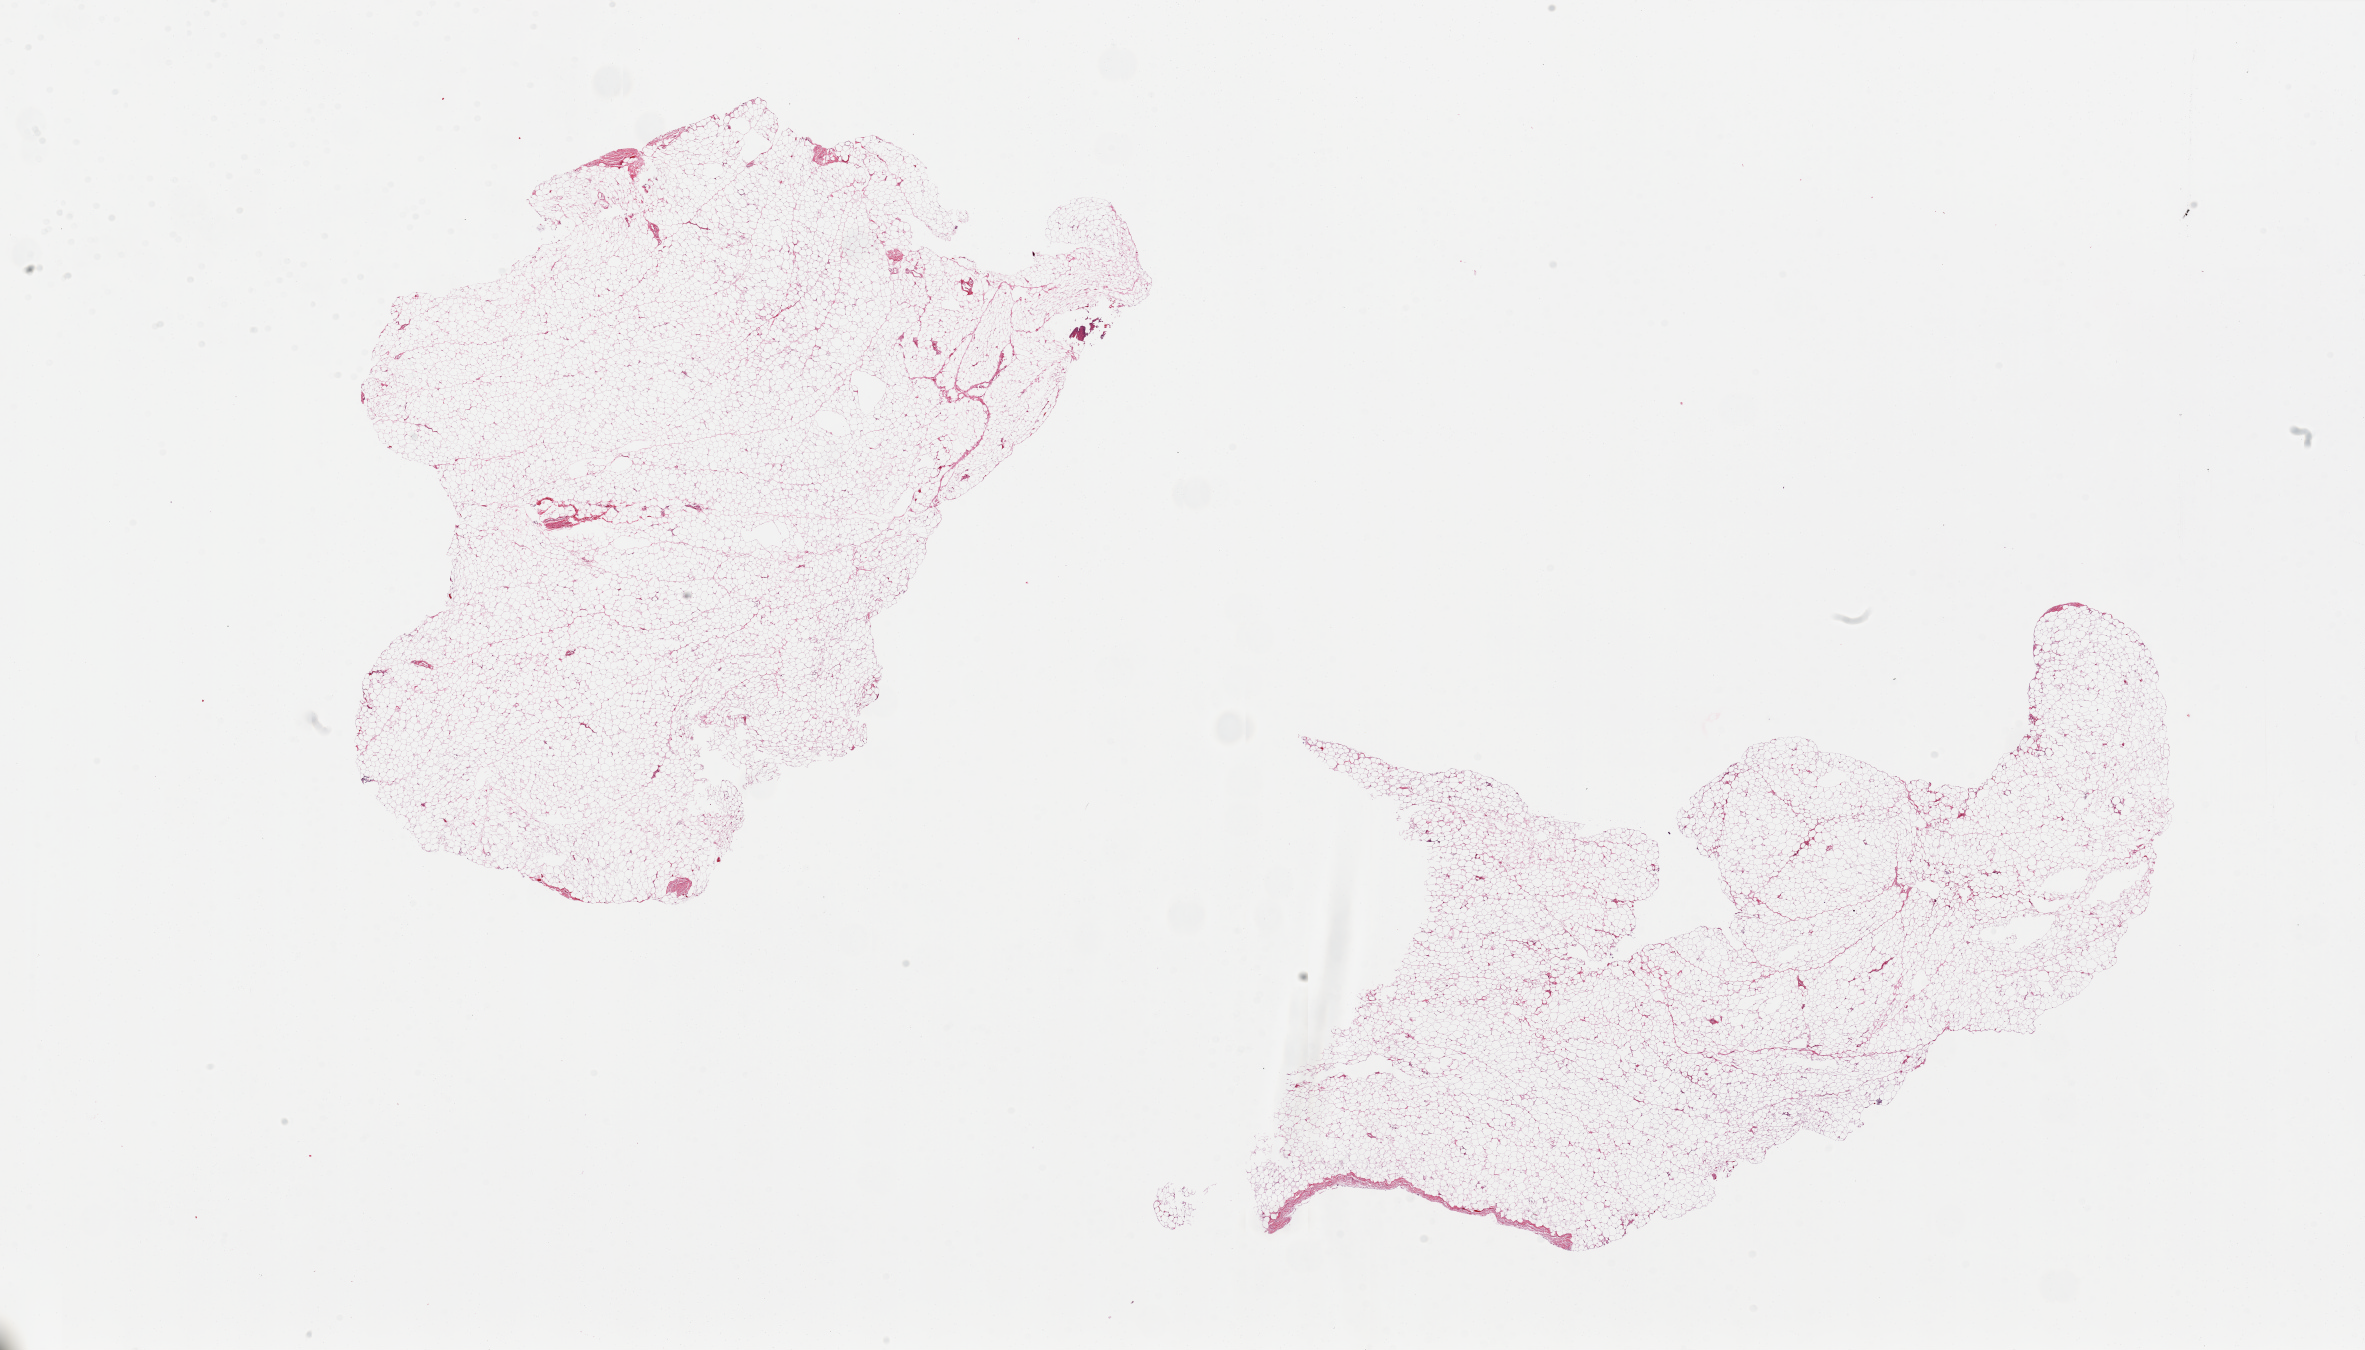
Digitized haematoxylin and eosin-stained section — a low-resolution overview of the entire scanned area, about 37.4 x 21.4 mm; PAXgene-fixed, paraffin-embedded tissue; sampled site (target tissue): omentum; tissue donor sample. Donor sex: male.
Review note (as recorded): 2 pieces.